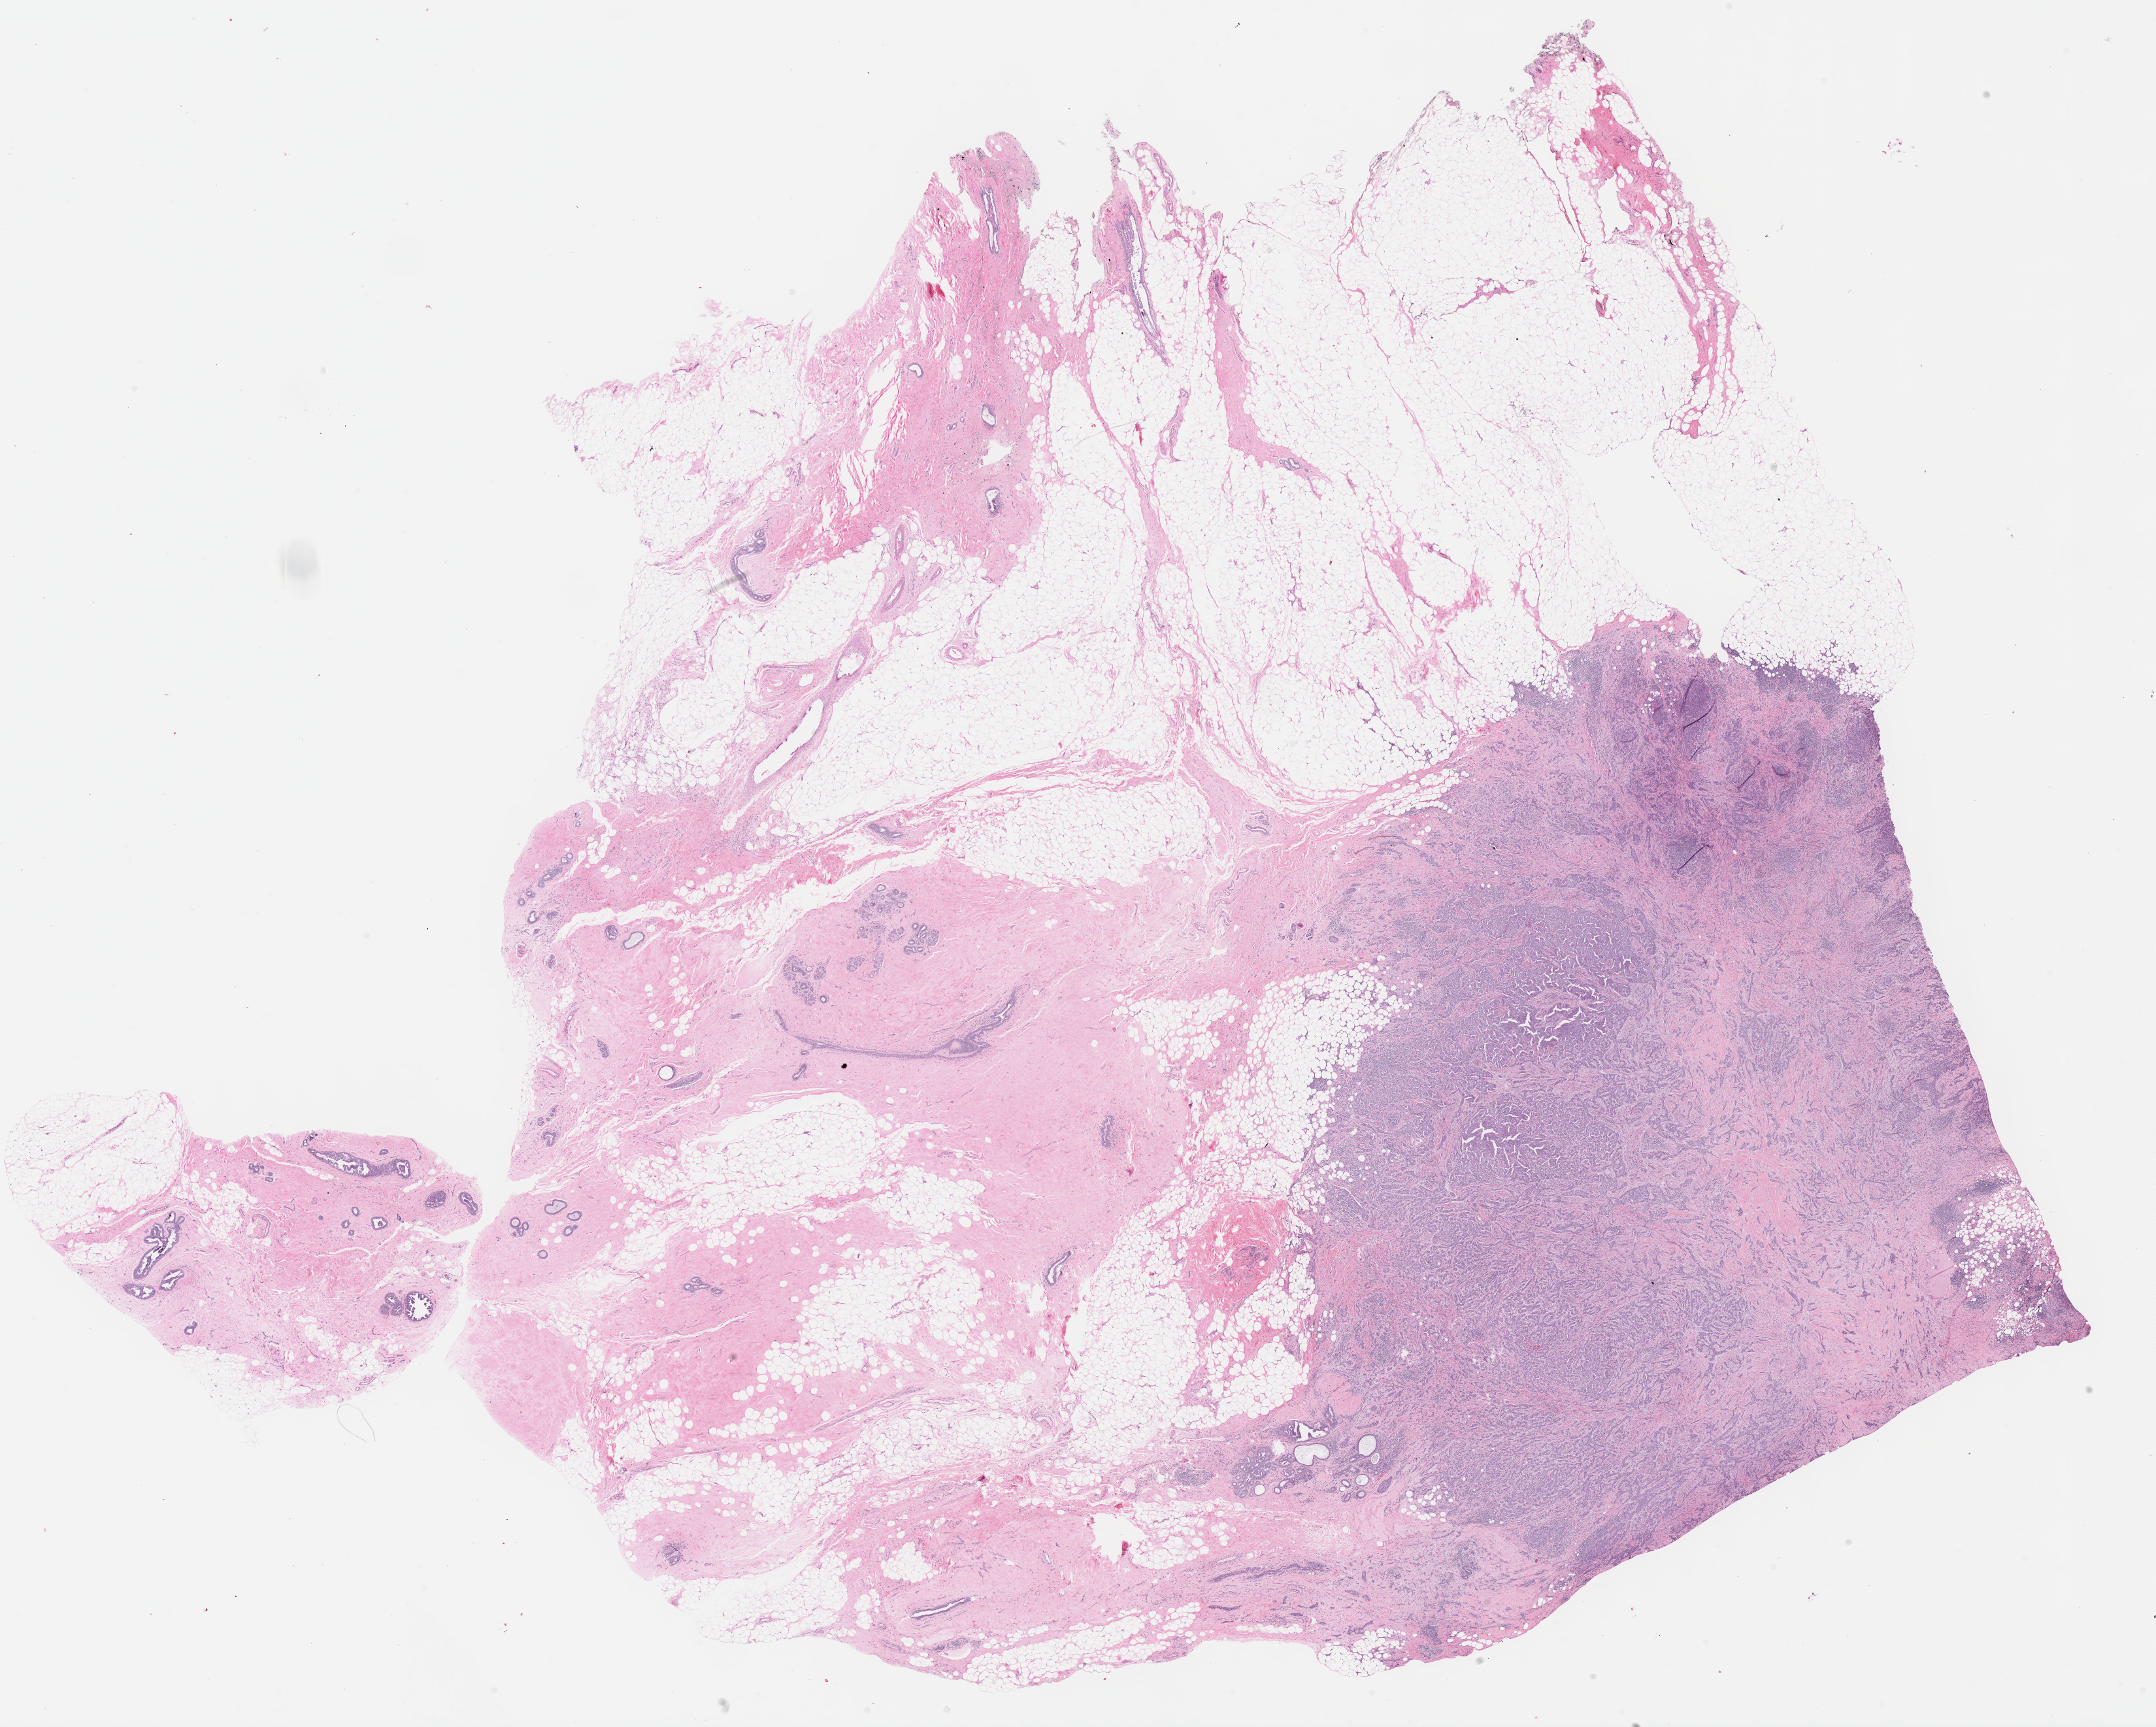
Whole-slide histology image, H&E-stained, whole scanned area (about 26.7 x 21.4 mm) shown as a low-resolution overview; FFPE section; sample: primary tumour, breast. Female, age 55 years at initial diagnosis.
Diagnosis: Infiltrating duct carcinoma, NOS.